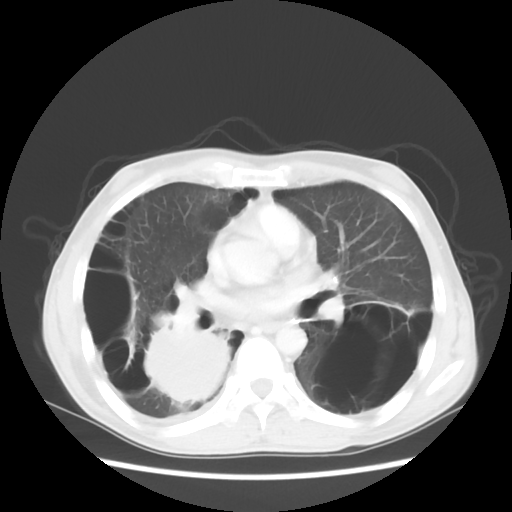
Chest CT, one axial slice; reconstruction kernel STANDARD; 140 kVp; lung window (W 1500 / L -600 HU); 5 mm slice thickness; 512 × 512 image matrix. Patient: male, 41 years. From the clinical record (not read from this slice): clinical TNM (as recorded): T4 N0 M1a; histopathological grade: G3.
Annotated regions visible in this slice (bounding box drawn by a radiologist):
- lung tumour (recorded histology: large cell carcinoma): bounding box [x1, y1, x2, y2] px = [139, 314, 238, 406]